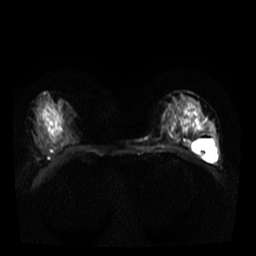
Breast MRI, one axial slice. Slice 20 of 40 in the series (ordered by position). Diffusion-weighted series; image 2 of 4 stored at this slice position (different b-values; order by instance number). 3 T. 256 × 256 image matrix, field of view 320 × 320 mm. Female patient.
Structures marked on this image (outlined manually by an expert reader):
- tumour on diffusion-weighted imaging: bounding box <198,155,201,158> (left, top, right, bottom; pixels)